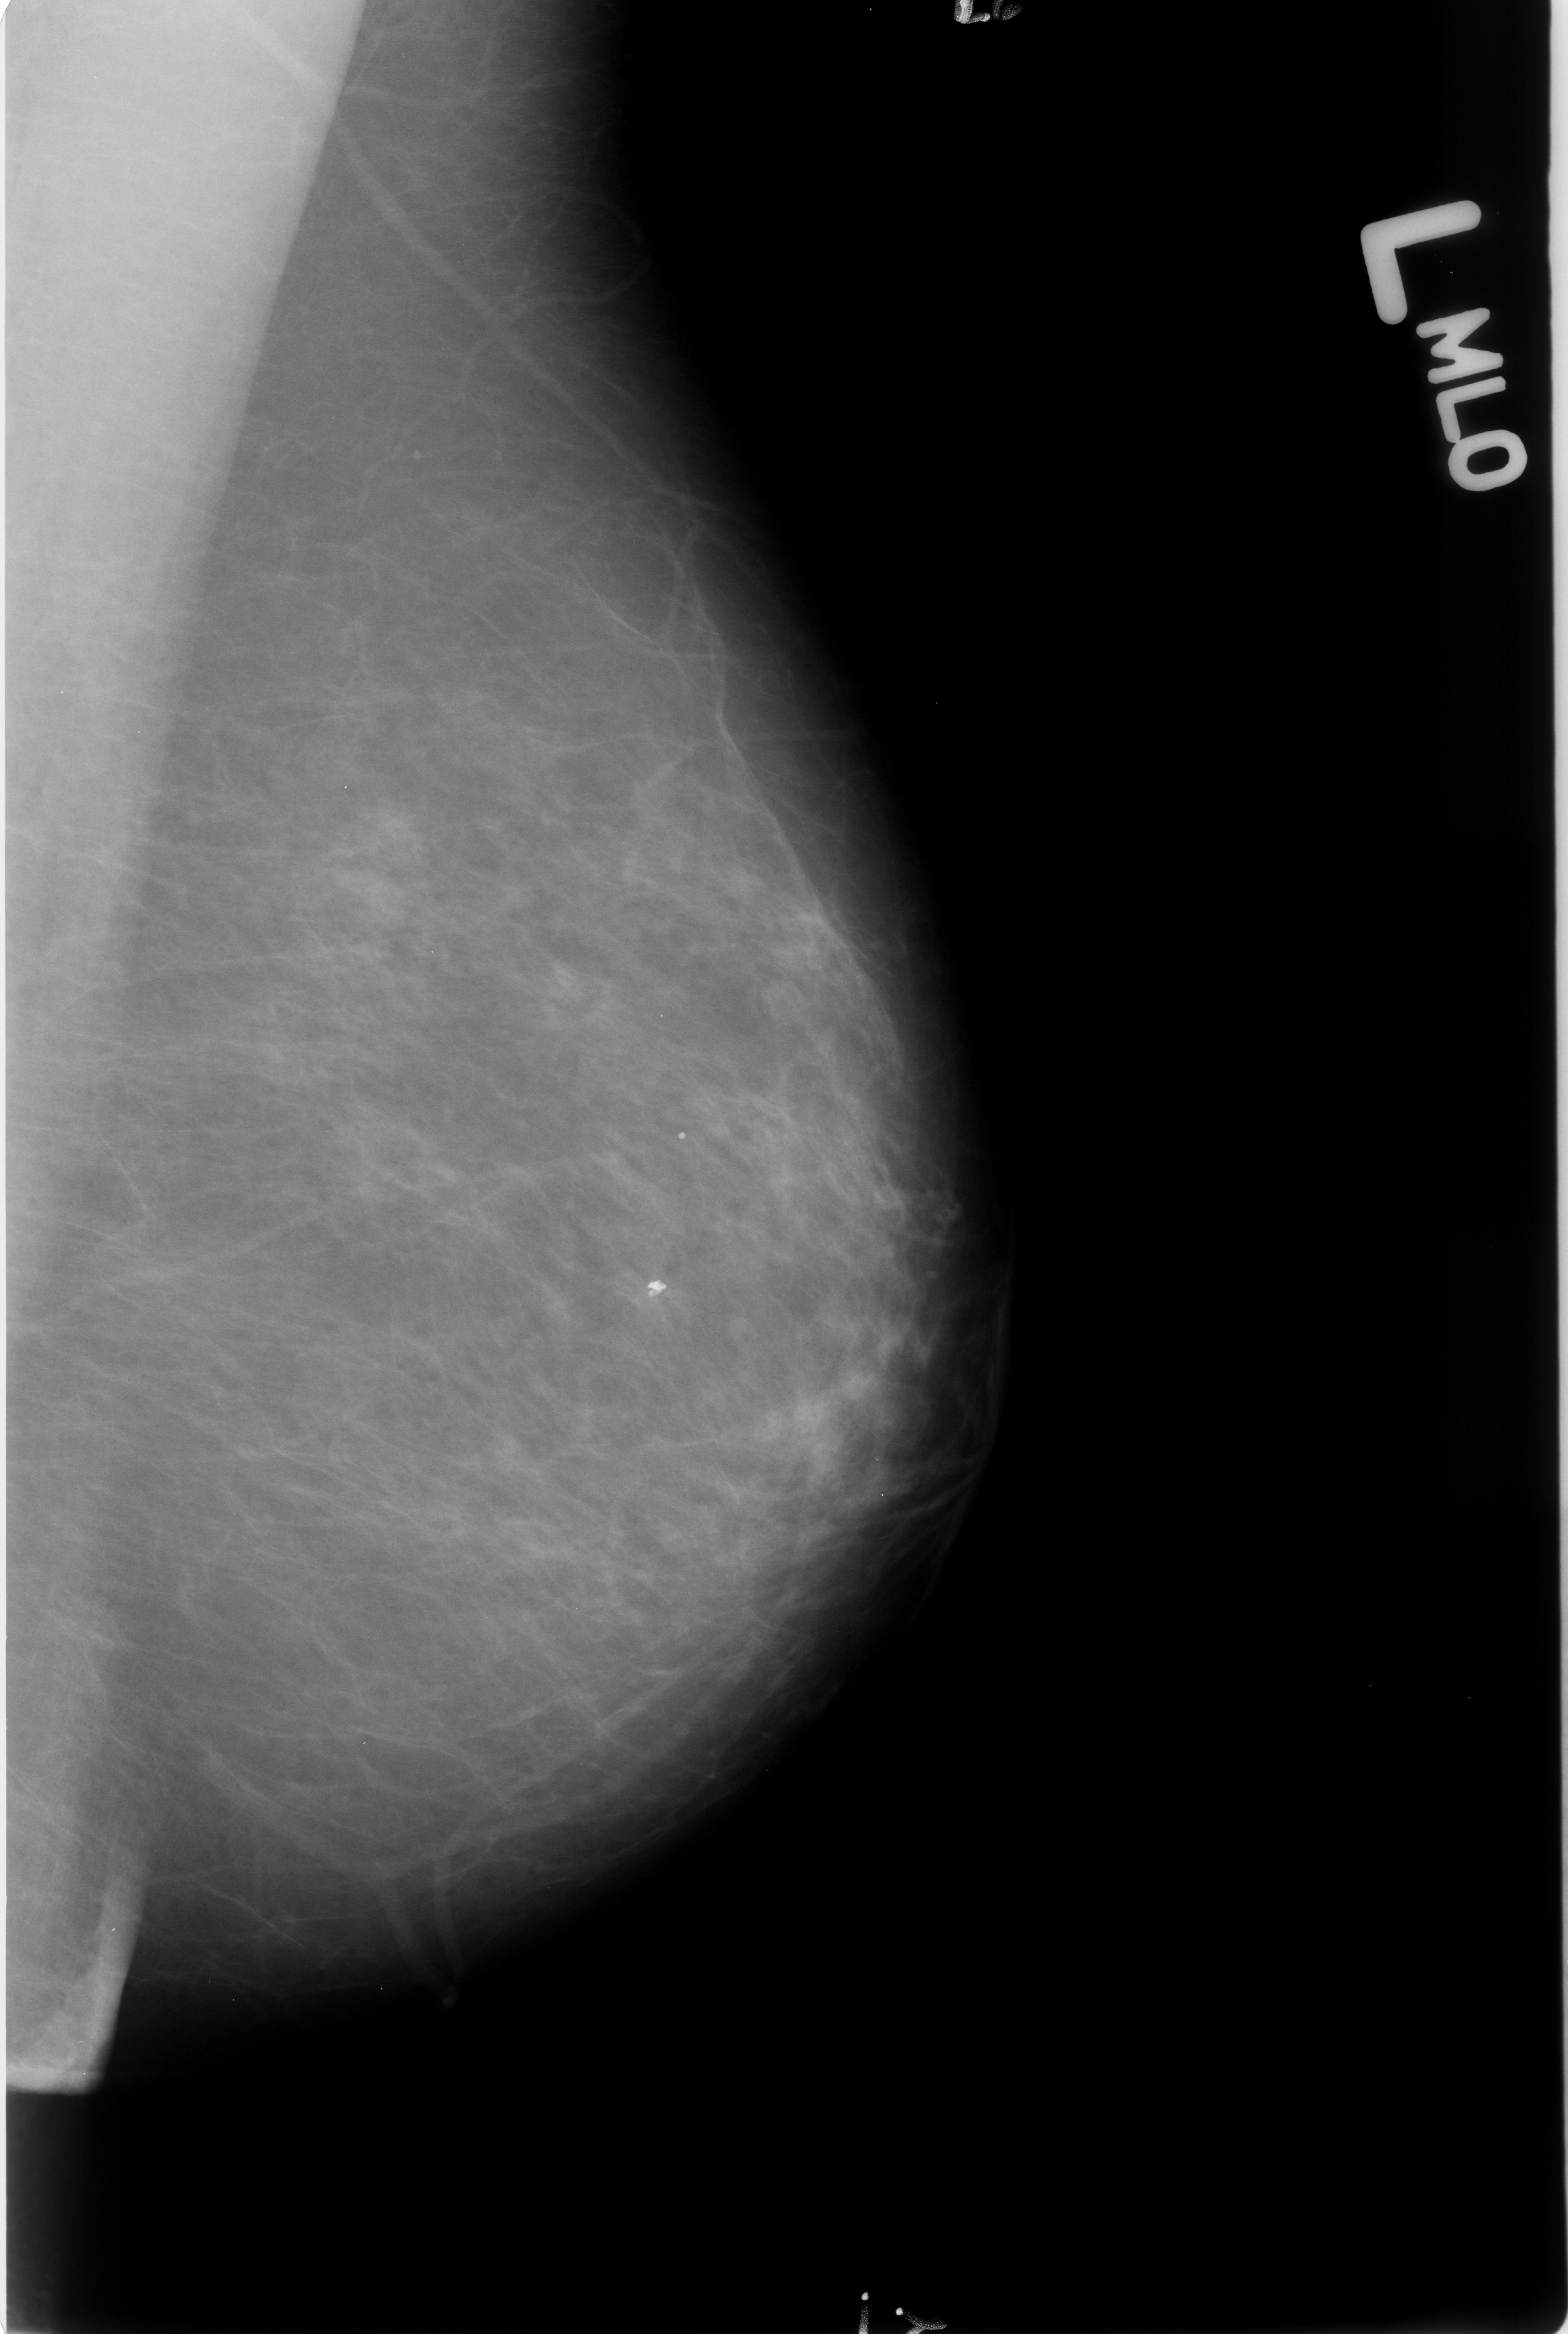
Digitized screen-film mammogram. Left breast. Mediolateral oblique (MLO) view. BI-RADS breast density category 1 (scale 1–4). 1568 × 2334 image matrix.
Marked abnormalities (boxes around the expert regions of interest):
- calcifications, morphology coarse; BI-RADS assessment category 2; subtlety rating 5 on a 1 (subtle) to 5 (obvious) scale; outcome (as recorded, no biopsy): benign without callback (not worked up further): bounding box <591,1237,733,1329> (left, top, right, bottom; pixels)